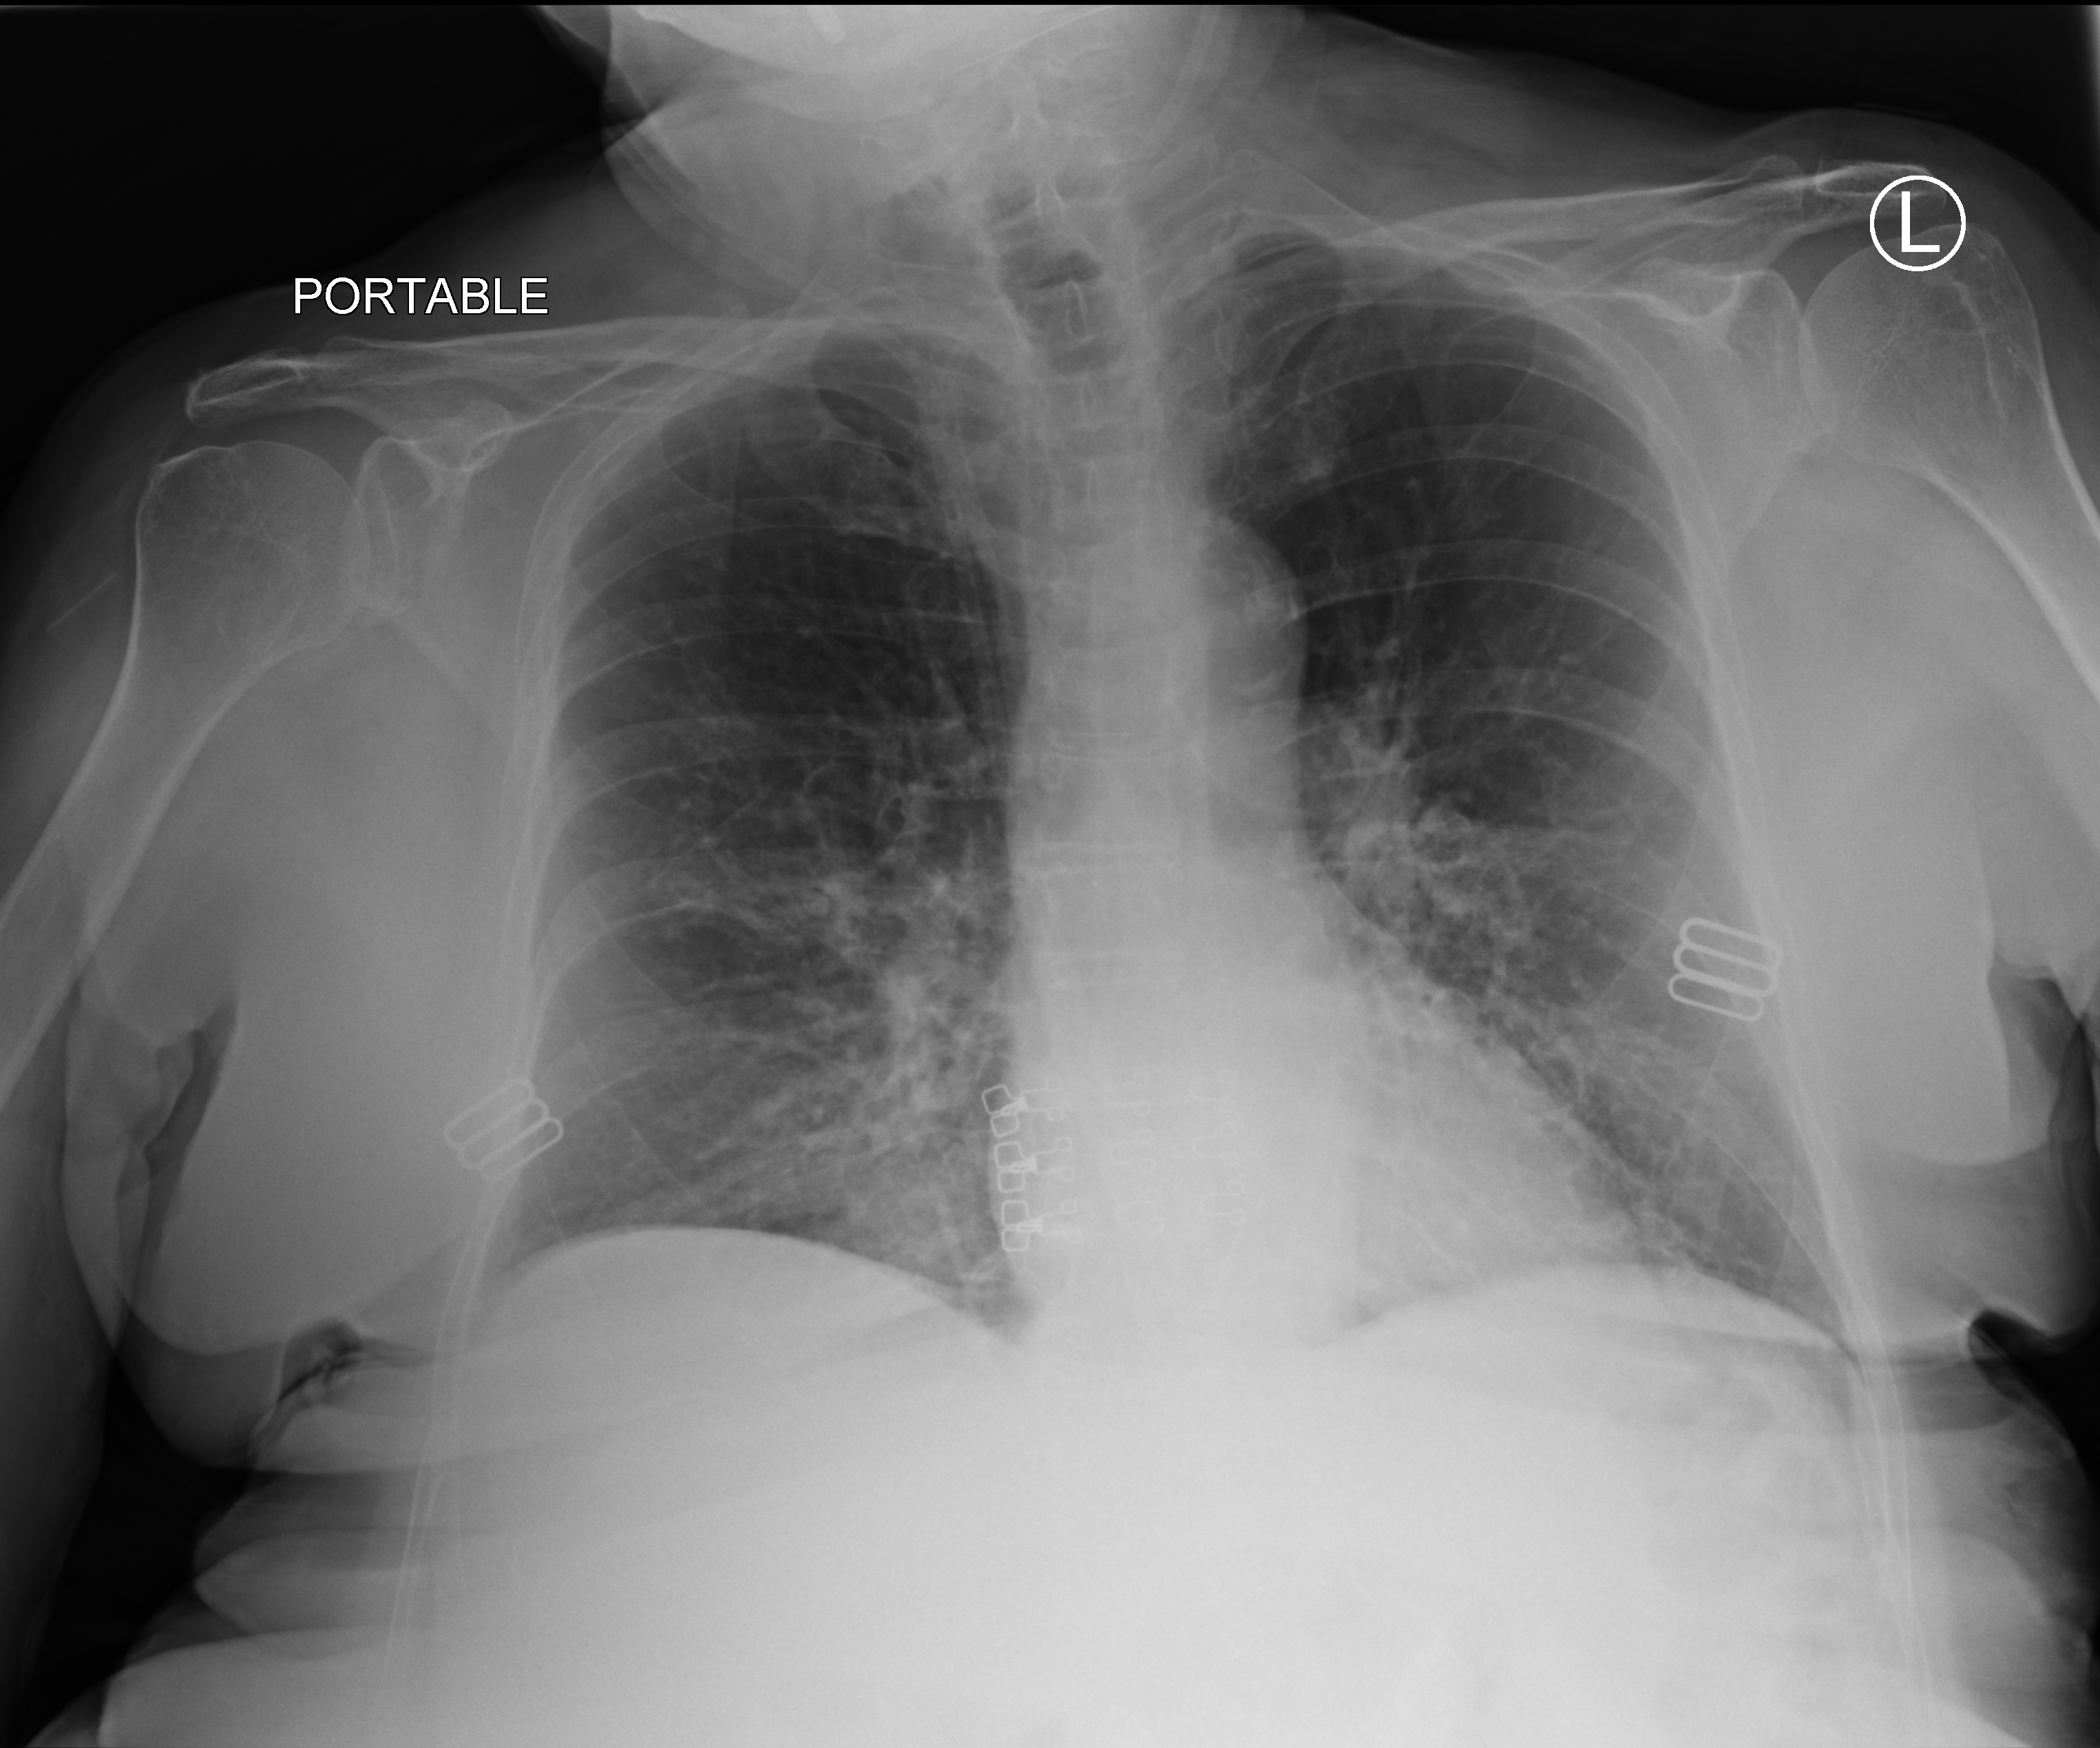
Chest X-ray (portable); anteroposterior (AP) projection. Female patient hospitalised with COVID-19, age 75–90 years.
Admission-level facts for this patient (not findings on this image; timing relative to this image not recorded):
- chronic kidney disease (admission record): no
- admitted to intensive care during this hospital stay: no
- mechanically ventilated during this hospital stay: no